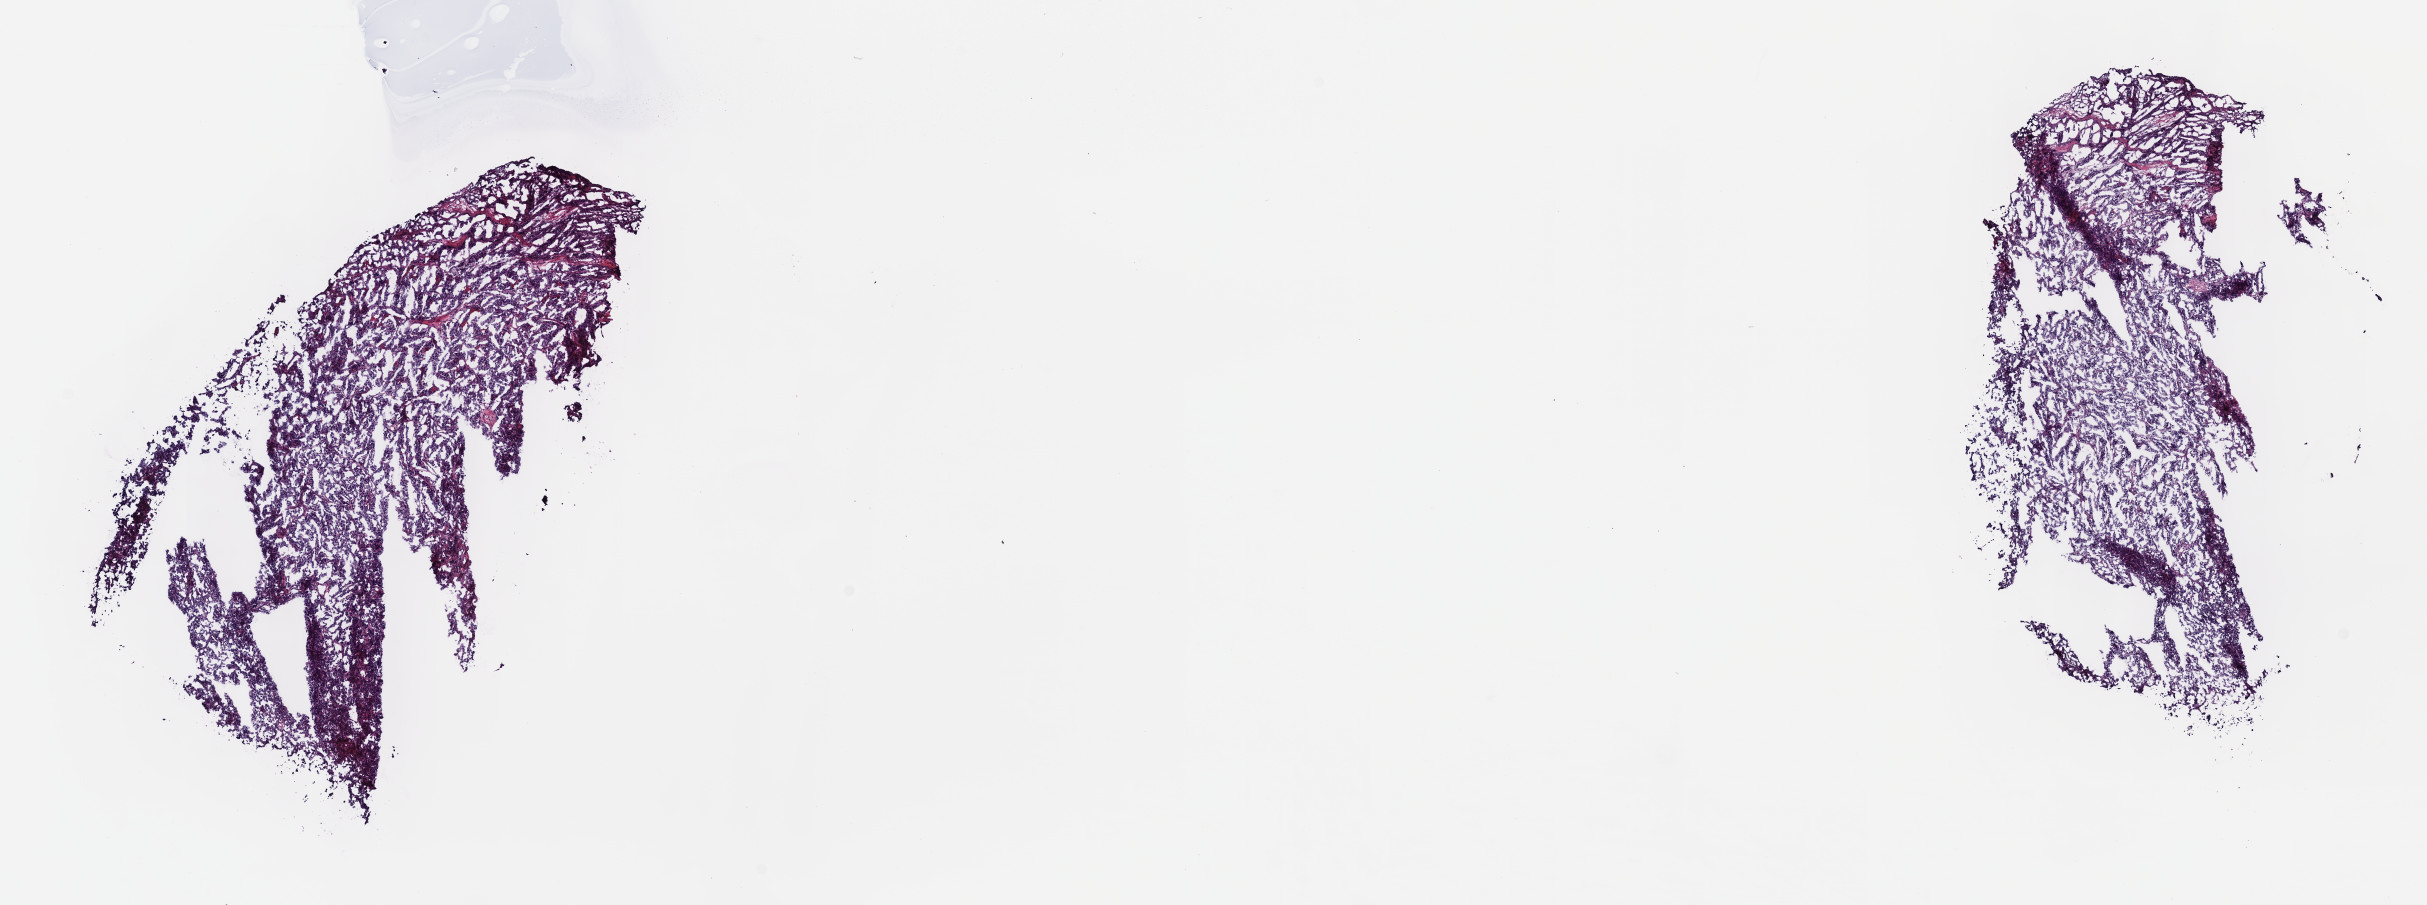
Digitized H&E-stained tissue section (whole slide), a low-resolution overview of the entire scanned area, about 19.6 x 7.3 mm (slide scanned at 40x), frozen section from the top of the tissue portion, sample: primary tumour, testis. Male patient; age at initial diagnosis 51 years. Composition of this section per pathologist review: tumour cells 100%, tumour nuclei 80%, normal cells 0%, stromal cells 0%, necrosis 0%. Infiltration values recorded for this section: lymphocyte infiltration 0%, monocyte infiltration 0%, neutrophil infiltration 0%.
AJCC pathologic stage: I (7th edition). Pathologic diagnosis: Seminoma, NOS. Laterality: right.